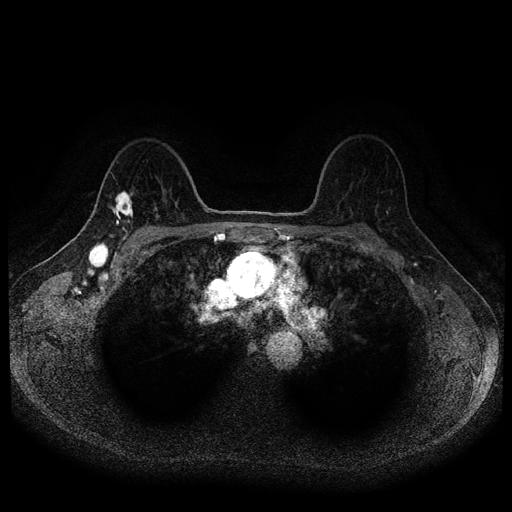
Breast MRI (dynamic contrast-enhanced, multi-phase), one axial slice. Slice 72 of 116 in the series (ordered by position). Dynamic contrast-enhanced series, time point 2 of 5 at this slice position (early post-contrast). 1.5 T. TE 2.6 ms, TR 5.4 ms. 2 mm slice thickness. 512 × 512 image matrix, field of view 340 × 340 mm. Female patient, age 49 years.
Annotated regions visible in this slice (semi-automatic segmentation, software-assisted and operator-edited):
- breast lesion (labelled 'tumour' in the annotation; benign lesions carry a separate 'benign' label): bounding box (x1, y1, x2, y2) in pixels: (108, 189, 133, 226)